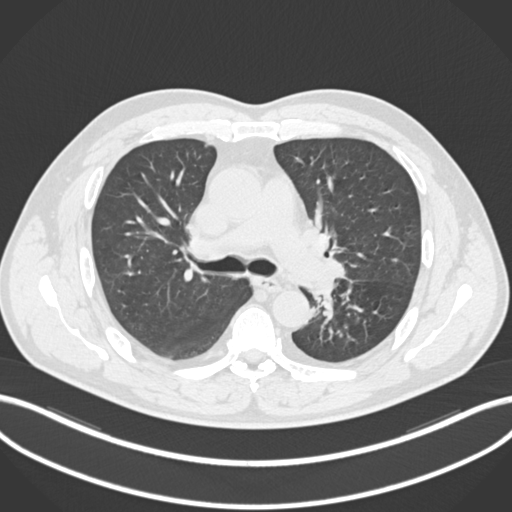
Chest CT, one axial slice; position 143 of 223 along the scan axis; lung window (W 1500 / L -600 HU); 1 mm slice thickness; 512 × 512 image matrix, field of view 400 × 400 mm. Male patient, age 50 years. Case-level facts recorded for this patient, not image findings: clinical TNM (as recorded): T2a N3 M0.
Structures marked on this image (rectangle marked by the reading radiologist):
- lung tumour (recorded histology: squamous cell carcinoma): bounding box <309,278,337,301> (left, top, right, bottom; pixels)